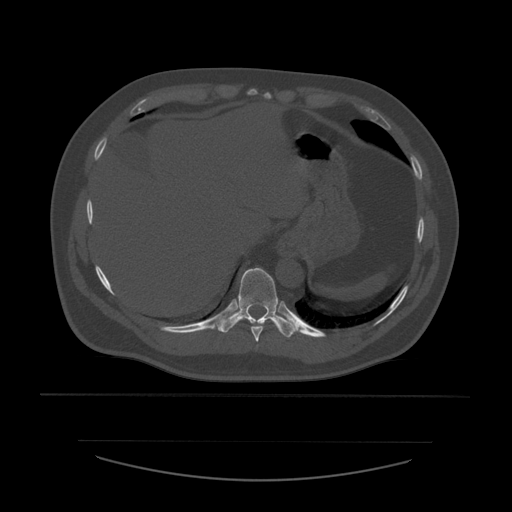
CT including the spine, one axial slice; position 304 of 532 along the scan axis; bone window (W 1800 / L 400 HU); 1.25 mm slice thickness; 512 × 512 image matrix. Patient age 44 years. From the clinical record (not read from this slice): primary cancer: soft tissue sarcoma.
Outlined on this slice (semi-automatically segmented with operator editing):
- T10 vertebra: bounding box <212,268,299,338> (left, top, right, bottom; pixels)
- T9 vertebra: <251,321,275,342>